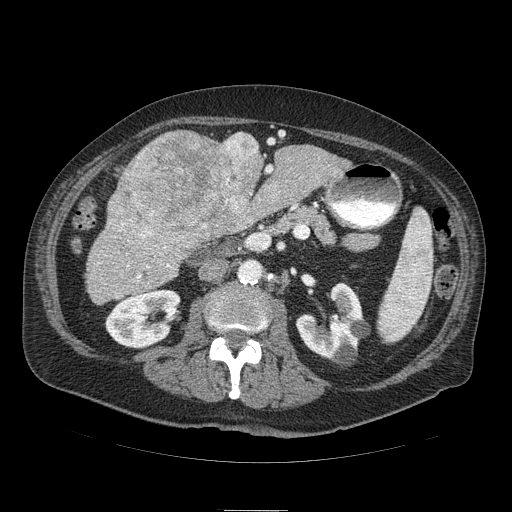
Contrast-enhanced abdominal CT (liver protocol), one axial slice. Position 34 of 103 along the scan axis. Soft-tissue window (W 400 / L 40 HU). 2.5 mm slice thickness. 512 × 512 image matrix, field of view 440 × 440 mm. From the clinical record (not read from this slice): diagnosis: hepatocellular carcinoma (patient treated with transarterial chemoembolisation; whether this scan precedes or follows treatment is not stated here); TNM stage (as recorded): Stage-IIIA; Child-Pugh class: B; tumour differentiation: well differentiated.
Outlined on this slice (semi-automatically segmented with operator editing):
- liver parenchyma outside the tumour (the mass and vessels are separate outlines, so this box may not span the whole liver): bounding box (x1, y1, x2, y2) in pixels: (92, 130, 349, 286)
- mass: (109, 130, 263, 253)
- liver vessels: (146, 166, 273, 268)